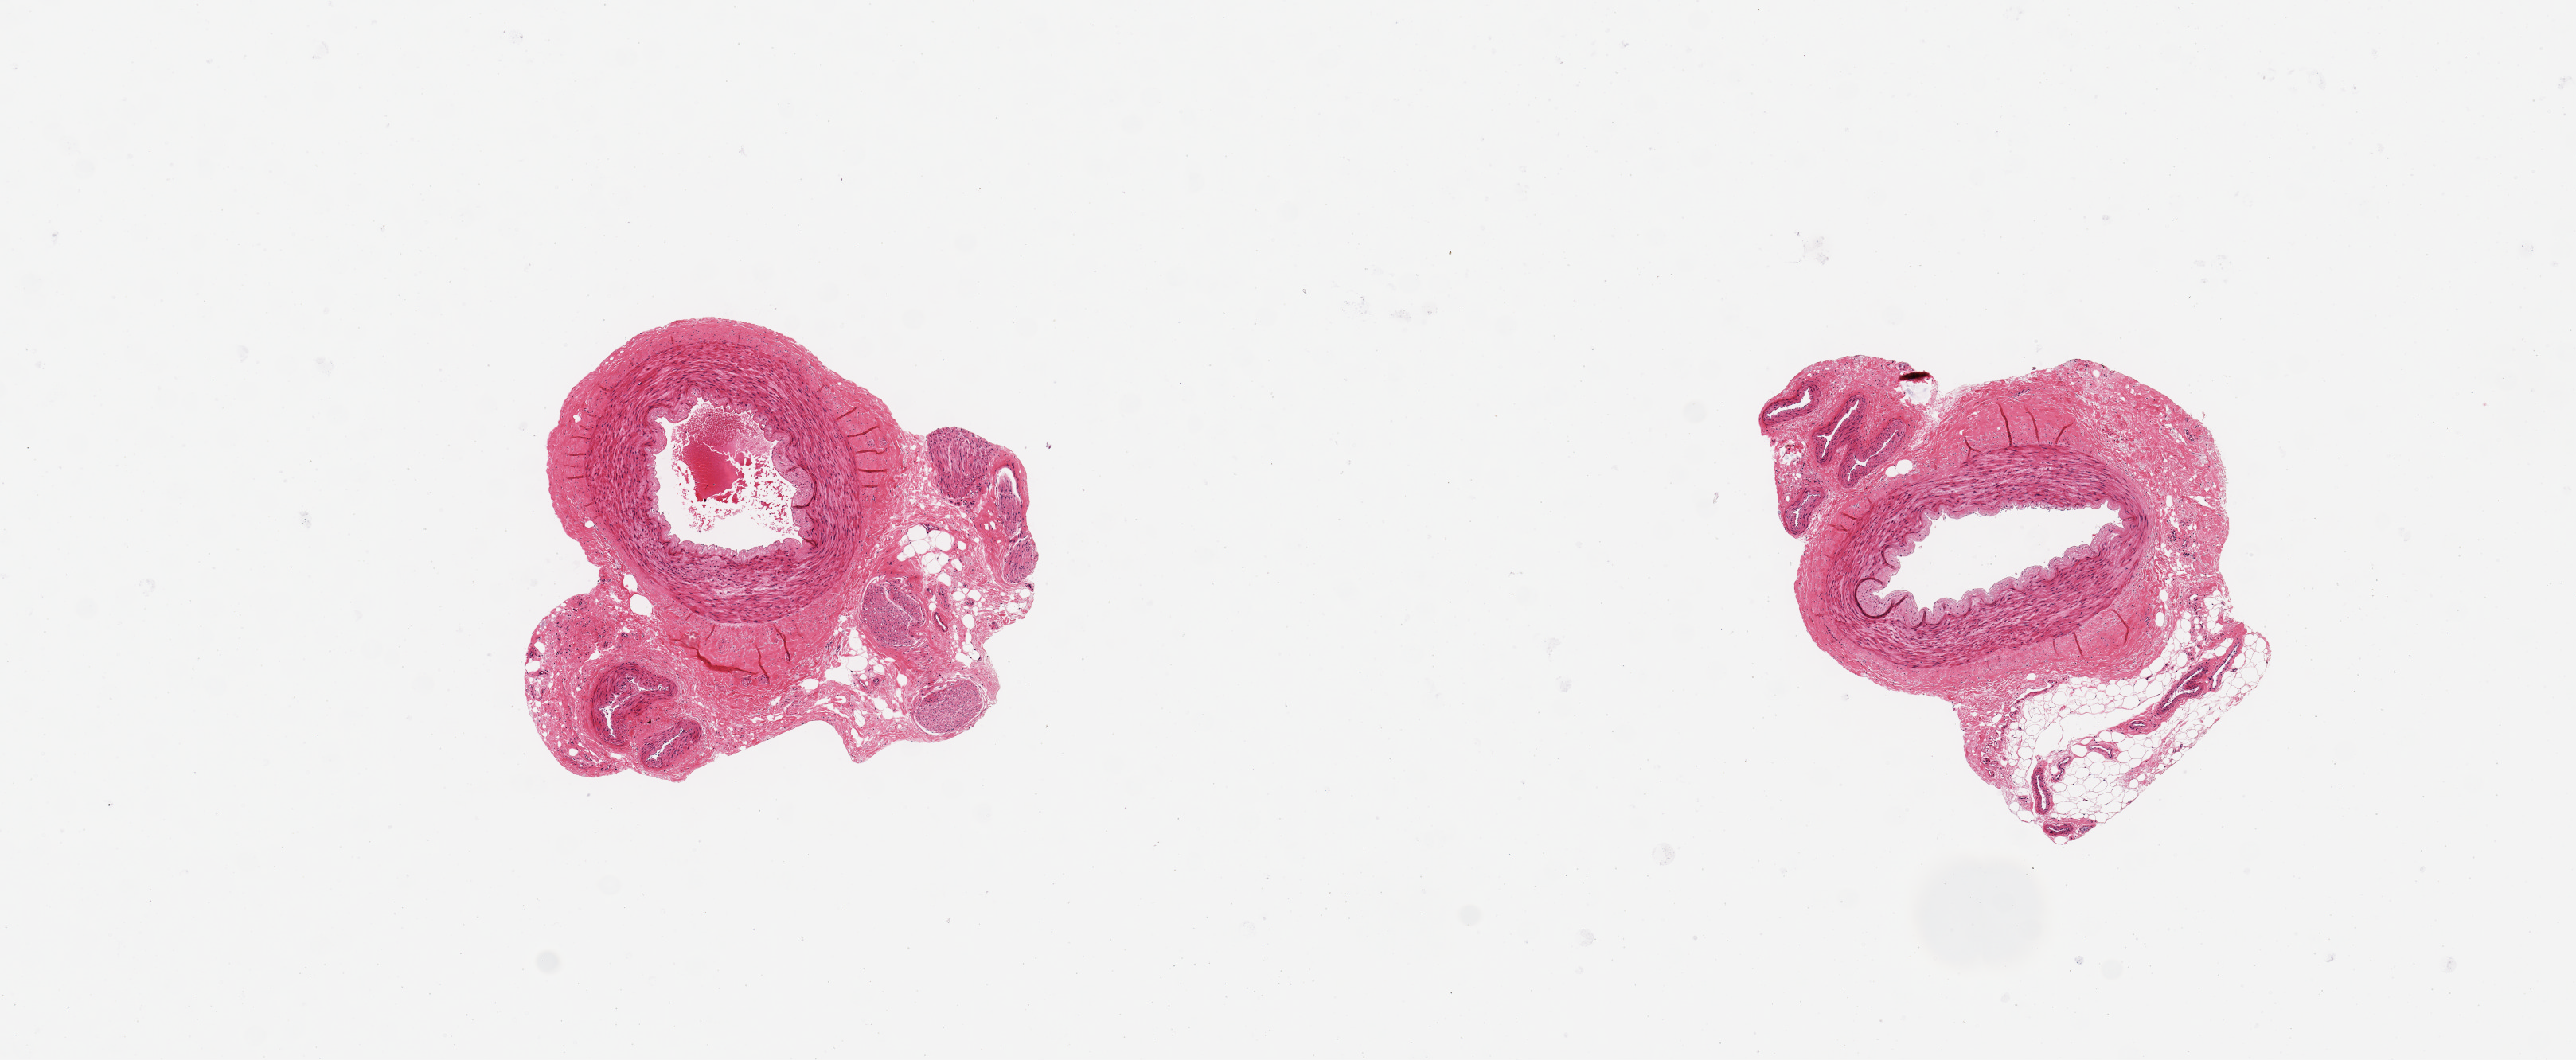
Digitized H&E-stained section, low-resolution overview of the scanned area, about 12.8 x 5.3 mm; PAXgene-fixed paraffin-embedded (PFPE) section; target tissue: tibial artery; tissue donor sample. Donor: female.
- reviewer comment on this tissue sample: 2 pieces, ~2 mm arteries with ~30% peripheral adipose, fibrous and nerve tissue